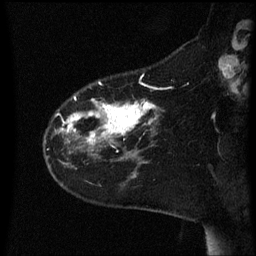
Breast MRI (dynamic contrast-enhanced), one sagittal slice. Slice 15 of 60 in the series (ordered by position). Dynamic contrast-enhanced series, image 2 of 3 at this slice position (ordered by acquisition). 1.5 T. TE 4.2 ms, TR 8.4 ms. 2.2 mm slice thickness. 256 × 256 image matrix, field of view 200 × 200 mm. Female patient, age 35 years. Case-level facts recorded for this patient, not image findings: setting: breast cancer imaged before/during neoadjuvant chemotherapy; receptor status: HER2-positive.
Annotated regions visible in this slice (semi-automatic segmentation, software-assisted and operator-edited):
- analysis volume of interest (the breast-tissue region the enhancement analysis was run in; not a lesion): bounding box [x1, y1, x2, y2] px = [45, 78, 165, 163]
- tumour enhancement mask (voxels above the 70 % enhancement threshold inside the analysis volume of interest): [60, 96, 156, 143]